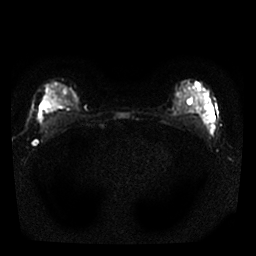
Breast MRI, one axial slice. Diffusion-weighted series; image 2 of 4 stored at this slice position (different b-values; order by instance number). 1.5 T. 4 mm slice thickness. 256 × 256 image matrix. Female patient.
Outlined on this slice (manually delineated by an expert):
- tumour on diffusion-weighted imaging: bounding box [x1, y1, x2, y2] px = [40, 90, 63, 109]